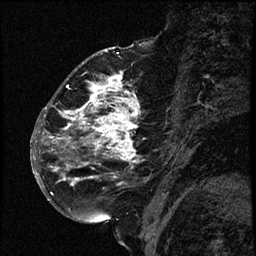
Breast MRI (dynamic contrast-enhanced), one sagittal slice; dynamic contrast-enhanced study with each time point stored as its own series, time point 2 of 3 at this slice position (early post-contrast, ordered by acquisition time); 1.5 T; TE 4.2 ms, TR 17.6 ms; 2 mm slice thickness; 256 × 256 image matrix, field of view 200 × 200 mm. Female patient. Case-level facts recorded for this patient, not image findings: setting: breast cancer imaged before/during neoadjuvant chemotherapy; receptor status: HER2-positive.
Outlined on this slice (semi-automatic segmentation, software-assisted and operator-edited):
- analysis volume of interest (the breast-tissue region the enhancement analysis was run in; not a lesion): bounding box <52,69,156,209> (left, top, right, bottom; pixels)
- tumour enhancement mask (voxels above the 100 % enhancement threshold inside the analysis volume of interest): <52,75,141,186>